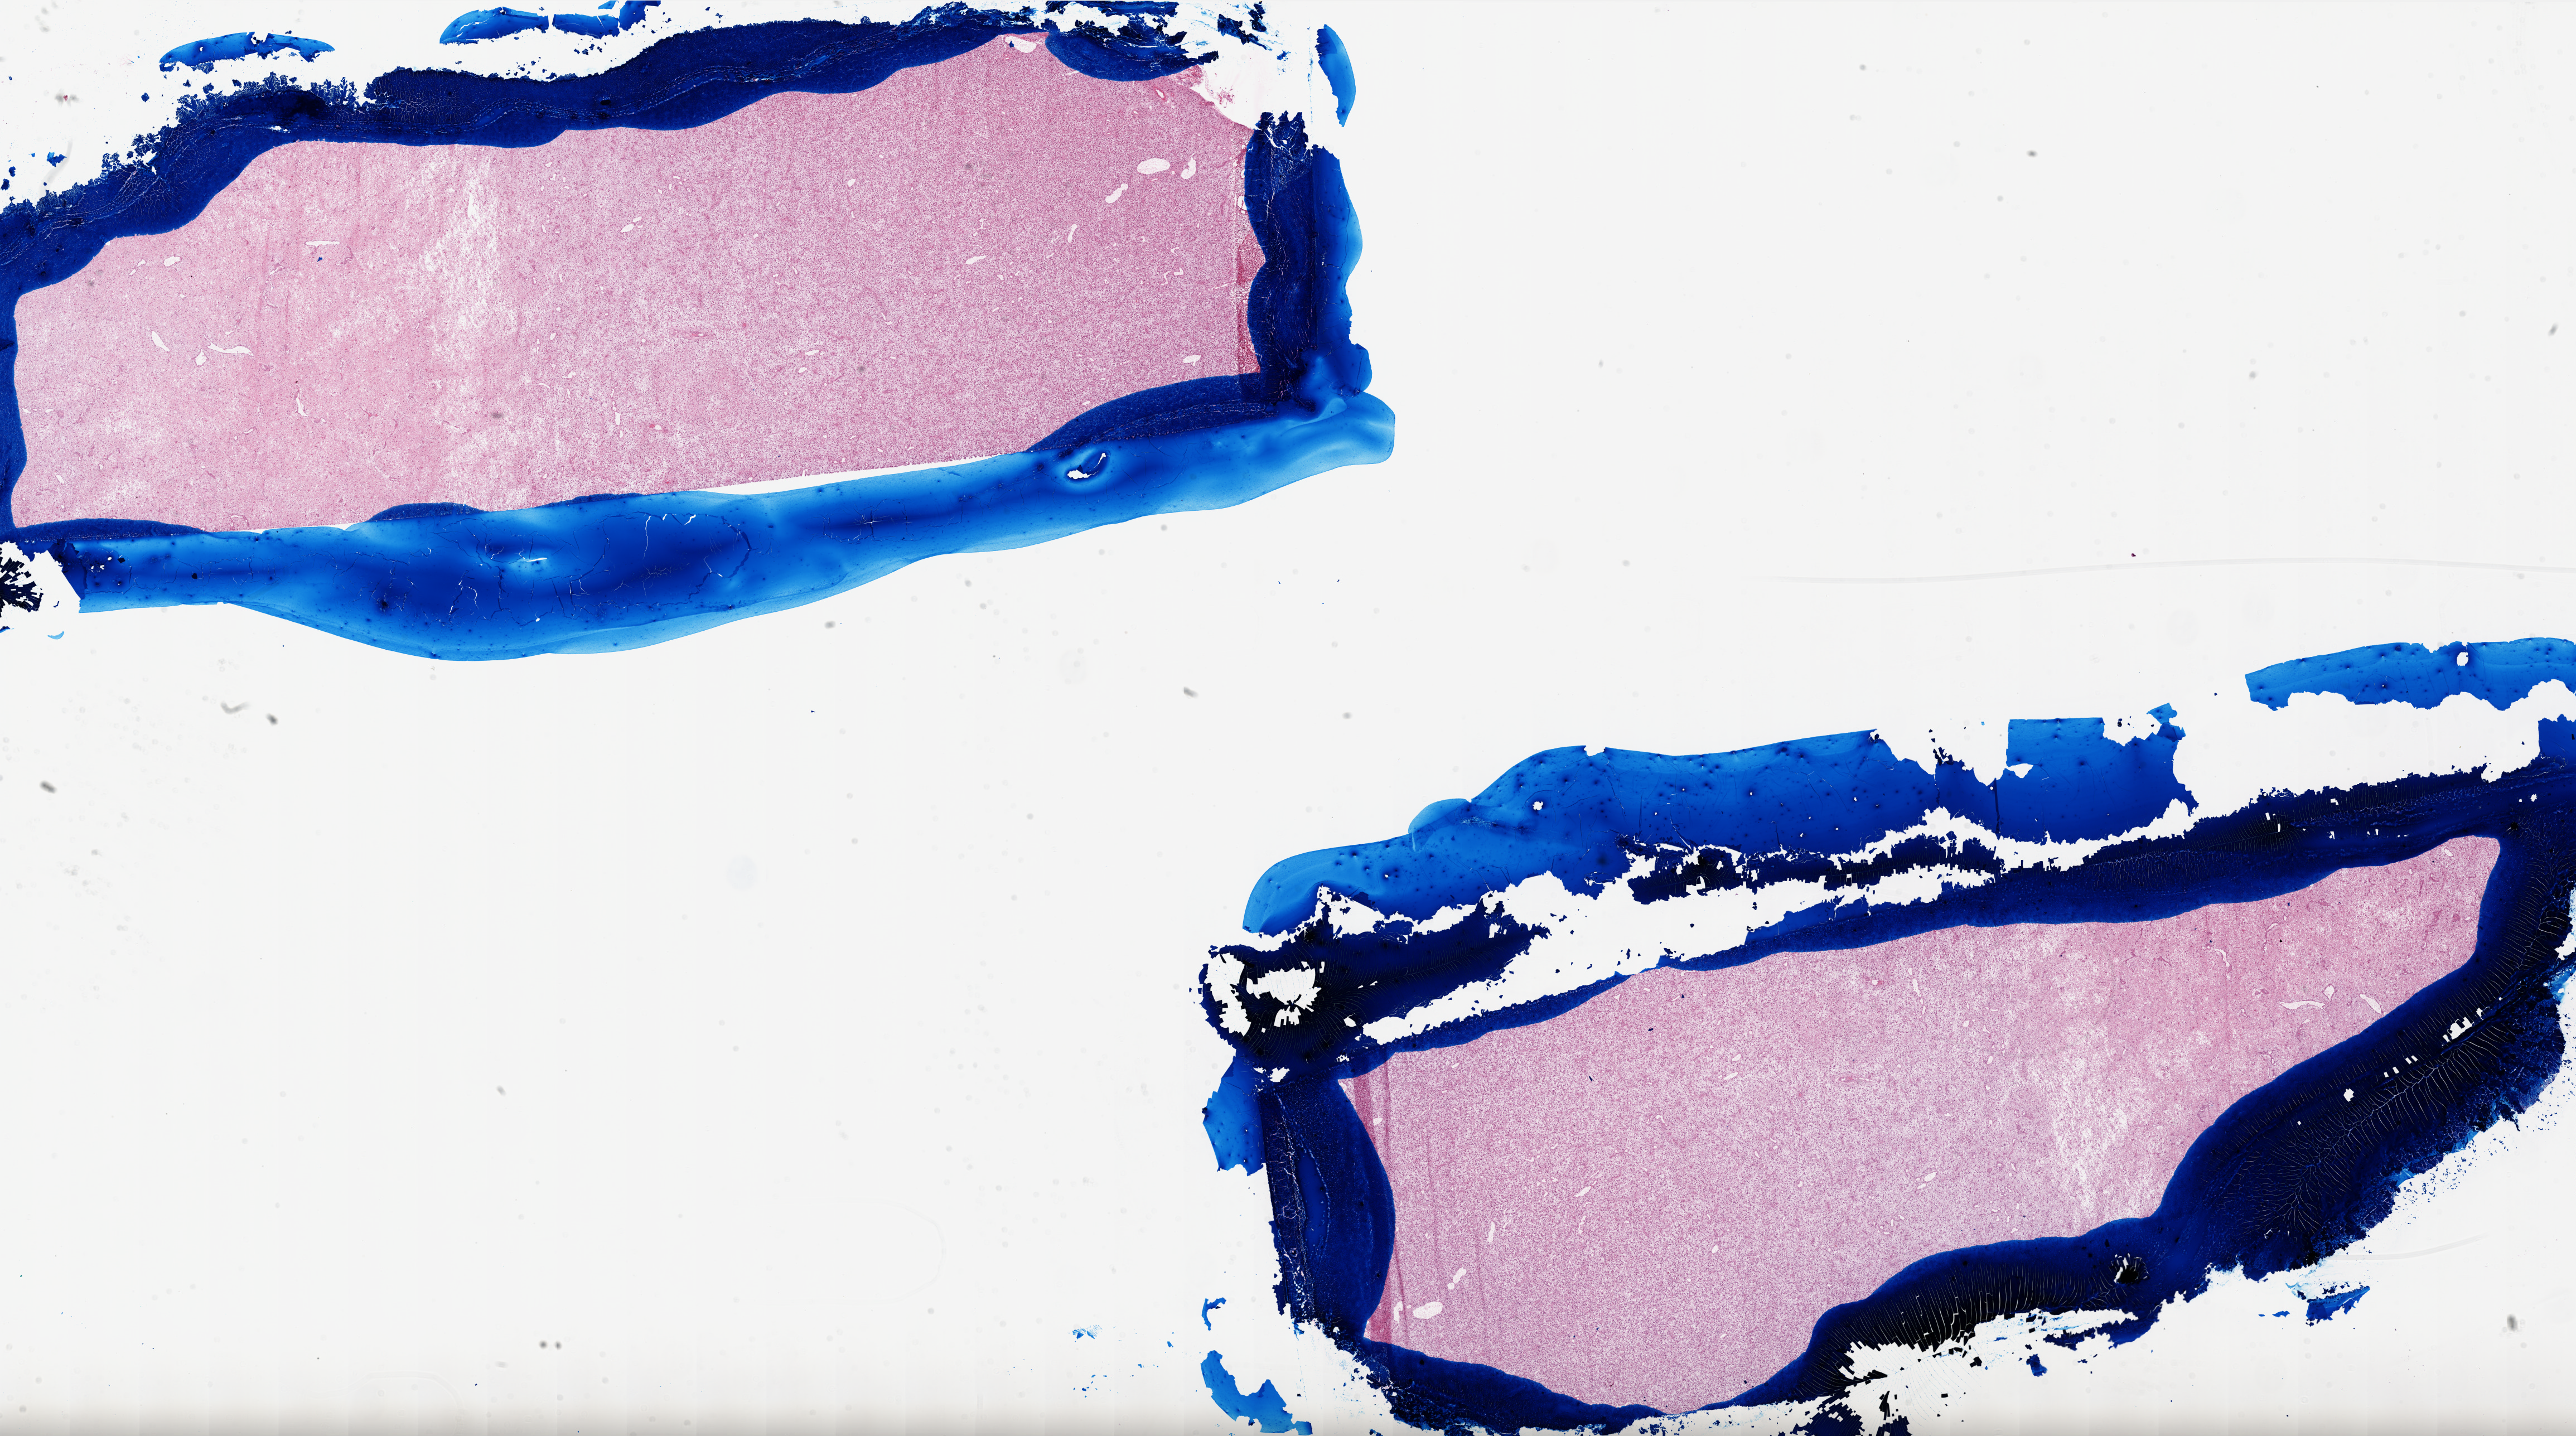
Whole-slide histology image, Hematoxylin and eosin (H&E) stained — low-resolution overview of the scanned area, about 37.0 x 20.6 mm (slide scanned at 20x), frozen section, primary tumour sample from the brain. Patient: female, age at initial diagnosis 48 years. Slide review estimates, as recorded: tumour cells 100%, tumour nuclei 100%, normal cells 0%, stromal cells 0%, necrosis 0%.
Diagnosis: Glioblastoma.